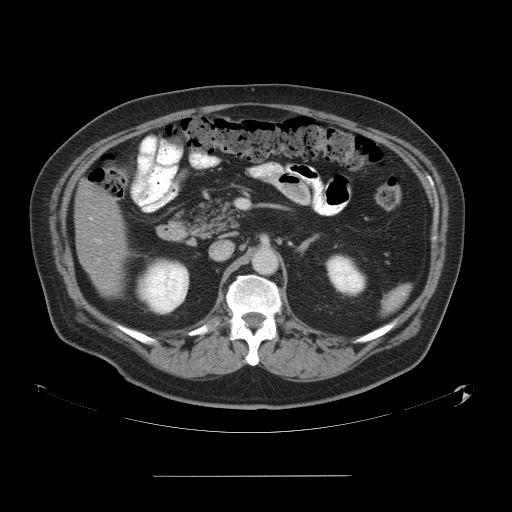
Contrast-enhanced abdominal CT, one axial slice; position 25 of 58 along the scan axis; 120 kVp; intravenous contrast given; soft-tissue window (W 400 / L 40 HU); 512 × 512 image matrix, field of view 480 × 480 mm. Male patient, age 63 years. From the clinical record (not read from this slice): diagnosis: colorectal cancer liver metastases, imaged before liver resection; multiple liver metastases: no; largest metastasis: 4.2 cm; disease in both lobes: no.
Outlined on this slice (expert manual segmentation):
- liver: bounding box [x1, y1, x2, y2] px = [75, 183, 125, 295]
- planned liver remnant (the part of the liver to remain after resection): [75, 183, 125, 295]
- portal vein (with intrahepatic branches): [90, 218, 100, 260]